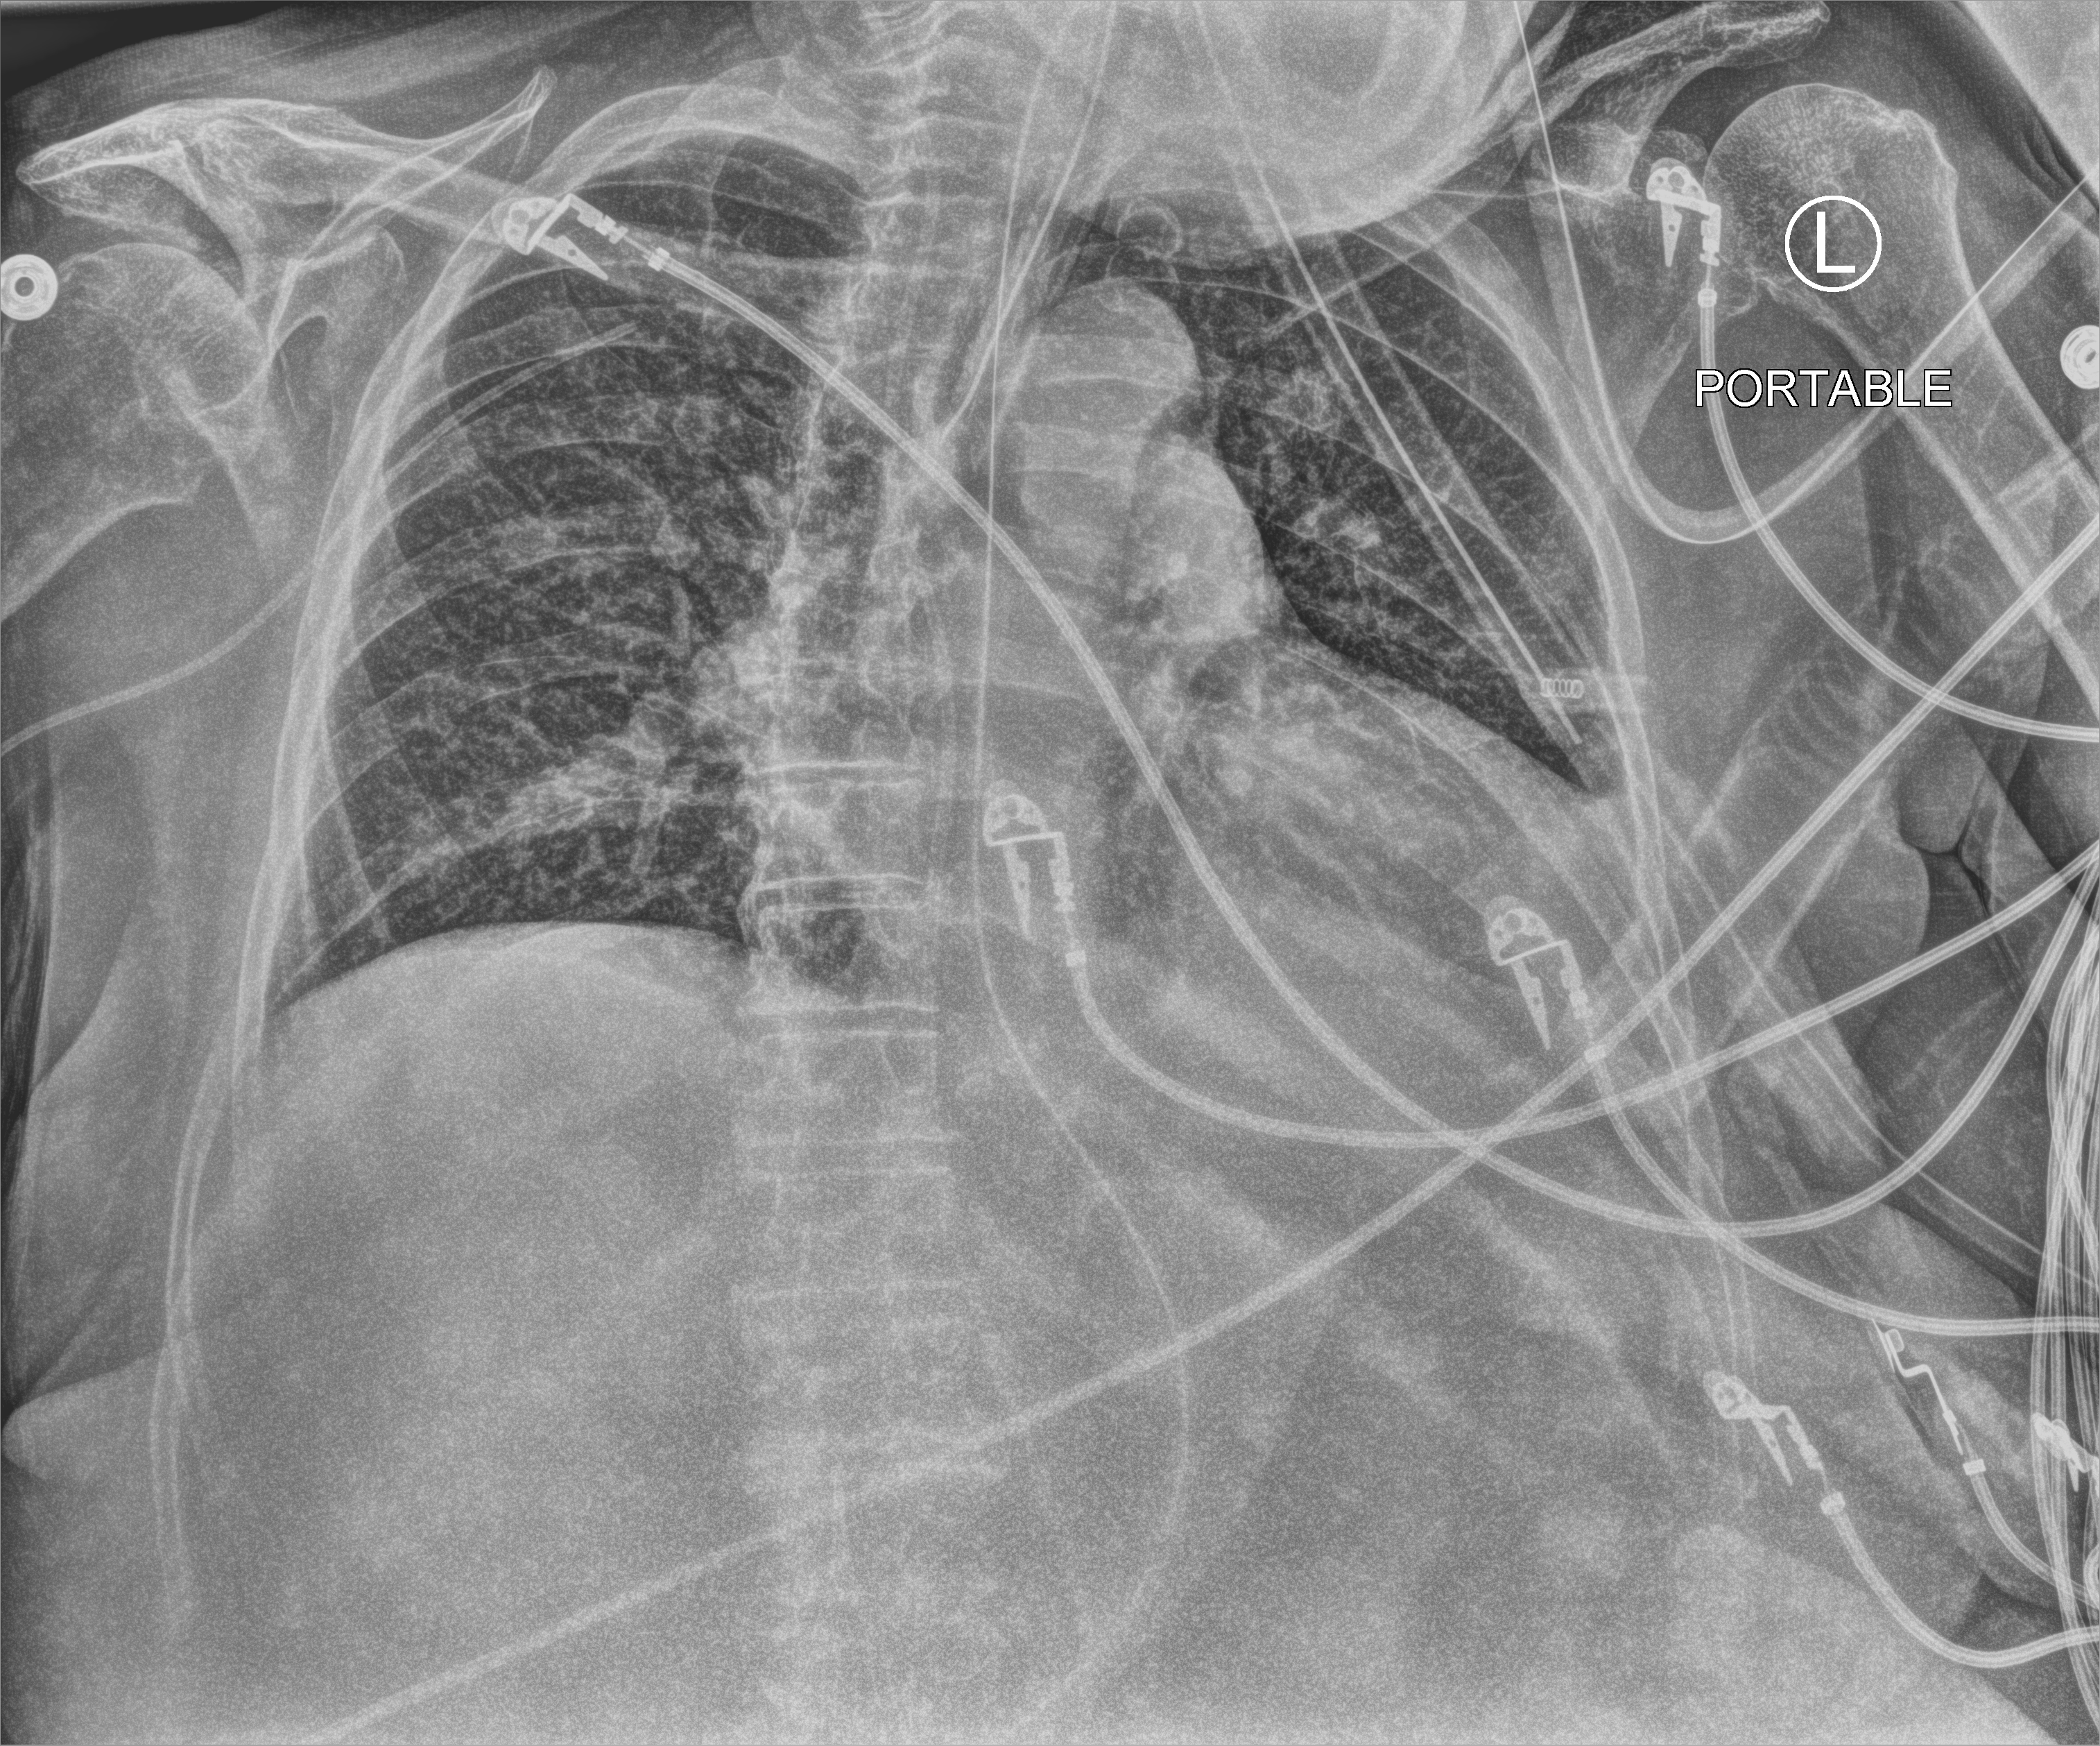
Portable chest radiograph, anteroposterior (AP) projection. Patient hospitalised with COVID-19; female, aged 75–90 years.
Hospital-stay facts (about this admission, not read from this image; timing relative to this image not recorded): admitted to intensive care during this hospital stay: yes.